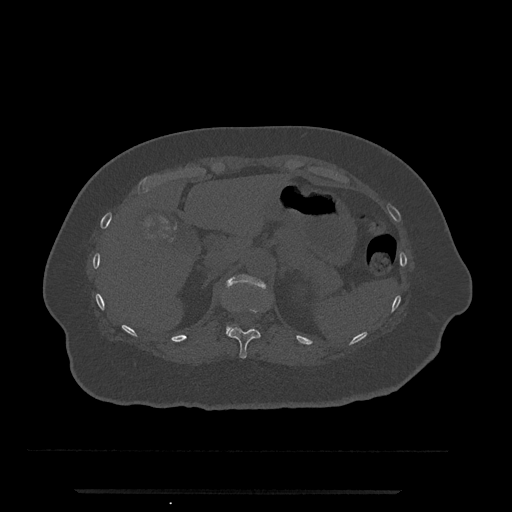
CT including the spine, one axial slice. Slice 207 of 797 in the series (ordered by position). Reconstruction kernel Br40s/3. 120 kVp. Bone window (W 1800 / L 400 HU). 0.5 mm slice thickness. 512 × 512 image matrix, field of view 440 × 440 mm. Patient: female, 51 years. Case-level facts recorded for this patient, not image findings: primary cancer: neuro.
Outlined on this slice (semi-automatically segmented with operator editing):
- T11 vertebra: bounding box [x1, y1, x2, y2] px = [227, 308, 261, 359]
- T12 vertebra: [226, 274, 266, 334]